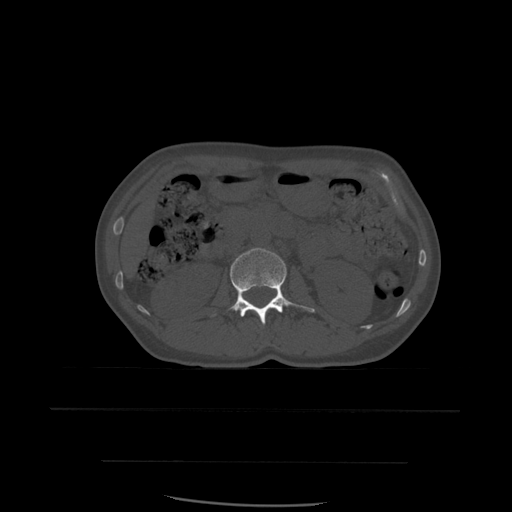
CT including the spine, one axial slice; position 225 of 574 along the scan axis; bone window (W 1800 / L 400 HU); 512 × 512 image matrix, field of view 392 × 392 mm. Patient age 48 years. Case-level facts recorded for this patient, not image findings: primary cancer: lung; vertebrae with lytic lesions (as recorded): T11.
Outlined on this slice (semi-automatically segmented with operator editing):
- L2 vertebra: bounding box [x1, y1, x2, y2] px = [212, 248, 316, 325]